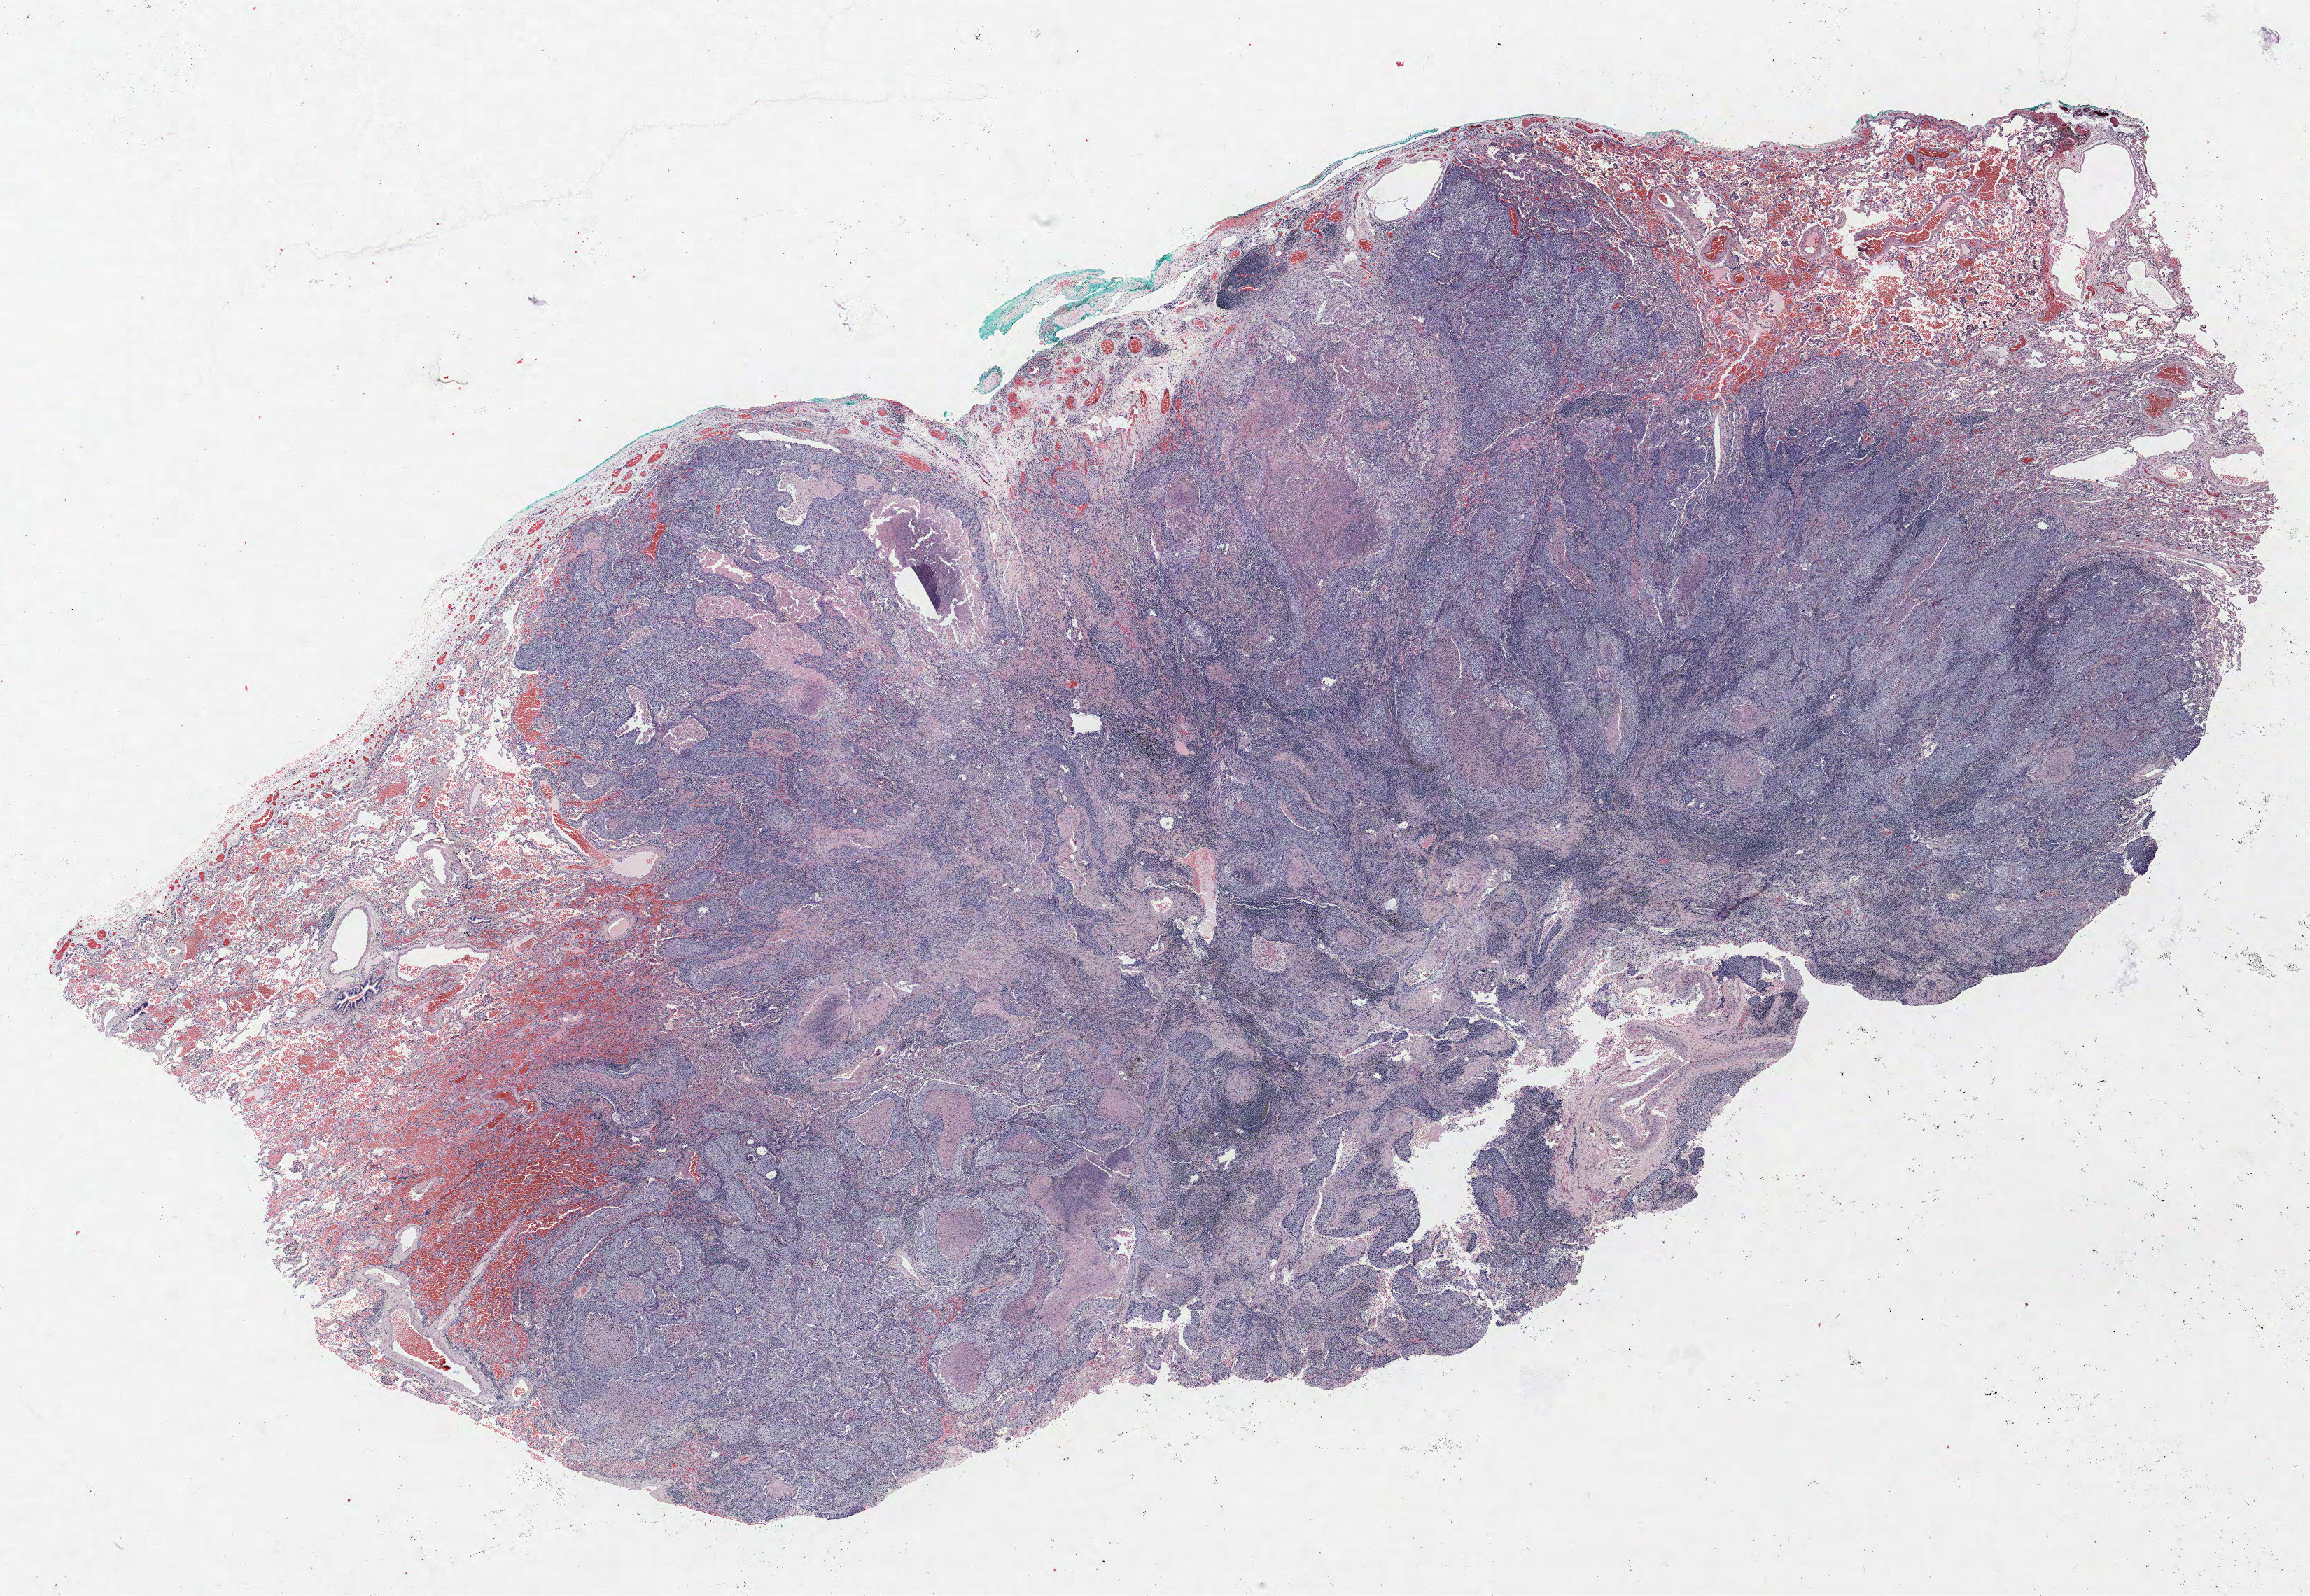
Hematoxylin and eosin (H&E) stained whole-slide image, low-resolution overview of the scanned area, about 26.4 x 18.2 mm; formalin-fixed paraffin-embedded (FFPE) section; lung. Male patient, aged 69 at enrolment. Current smoker at enrolment. Grade: moderately differentiated (G2).
ICD-O-3 topography: lower lobe of lung (C34.3). Stage (AJCC 6th edition): IA. Primary tumour location (clinical record): right lower lobe. Tumour size (pathology): 23 mm. Participant's lung-cancer diagnosis: Squamous cell carcinoma, NOS.